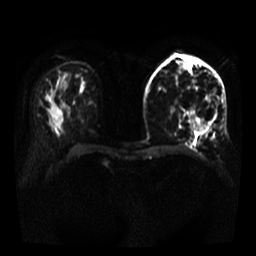
Breast MRI, one axial slice. Slice 20 of 35 in the series (ordered by position). Diffusion-weighted series; image 2 of 4 stored at this slice position (different b-values; order by instance number). 3 T. 5 mm slice thickness. 256 × 256 image matrix, field of view 320 × 320 mm. Female patient.
Annotated regions visible in this slice (outlined manually by an expert reader):
- tumour on diffusion-weighted imaging: bounding box (x1, y1, x2, y2) in pixels: (194, 116, 212, 133)